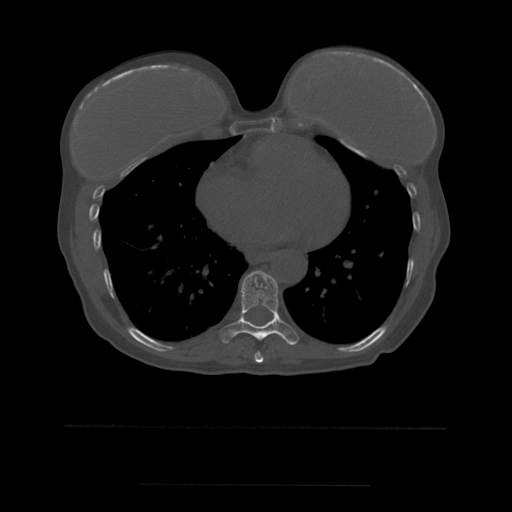
CT including the spine, one axial slice. Slice 322 of 544 in the series (ordered by position). Bone window (W 1800 / L 400 HU). 1.25 mm slice thickness. 512 × 512 image matrix, field of view 350 × 350 mm. Patient age 58 years. From the clinical record (not read from this slice): primary cancer: lung.
Structures marked on this image (semi-automatically segmented with operator editing):
- T8 vertebra: bounding box [x1, y1, x2, y2] px = [255, 352, 264, 363]
- T9 vertebra: [223, 271, 299, 345]